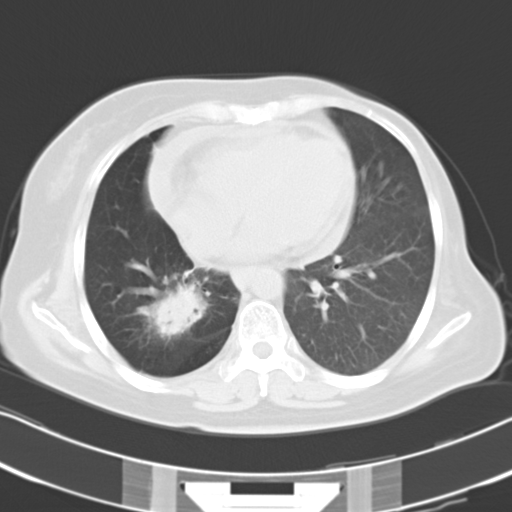
Chest CT, one axial slice; reconstruction kernel B40f; 120 kVp; lung window (W 1500 / L -600 HU); 512 × 512 image matrix. Female patient, age 53 years. From the clinical record (not read from this slice): clinical TNM (as recorded): T2b N1 M0.
Annotated regions visible in this slice (rectangle marked by the reading radiologist):
- lung tumour (recorded histology: adenocarcinoma): bounding box <146,285,207,335> (left, top, right, bottom; pixels)